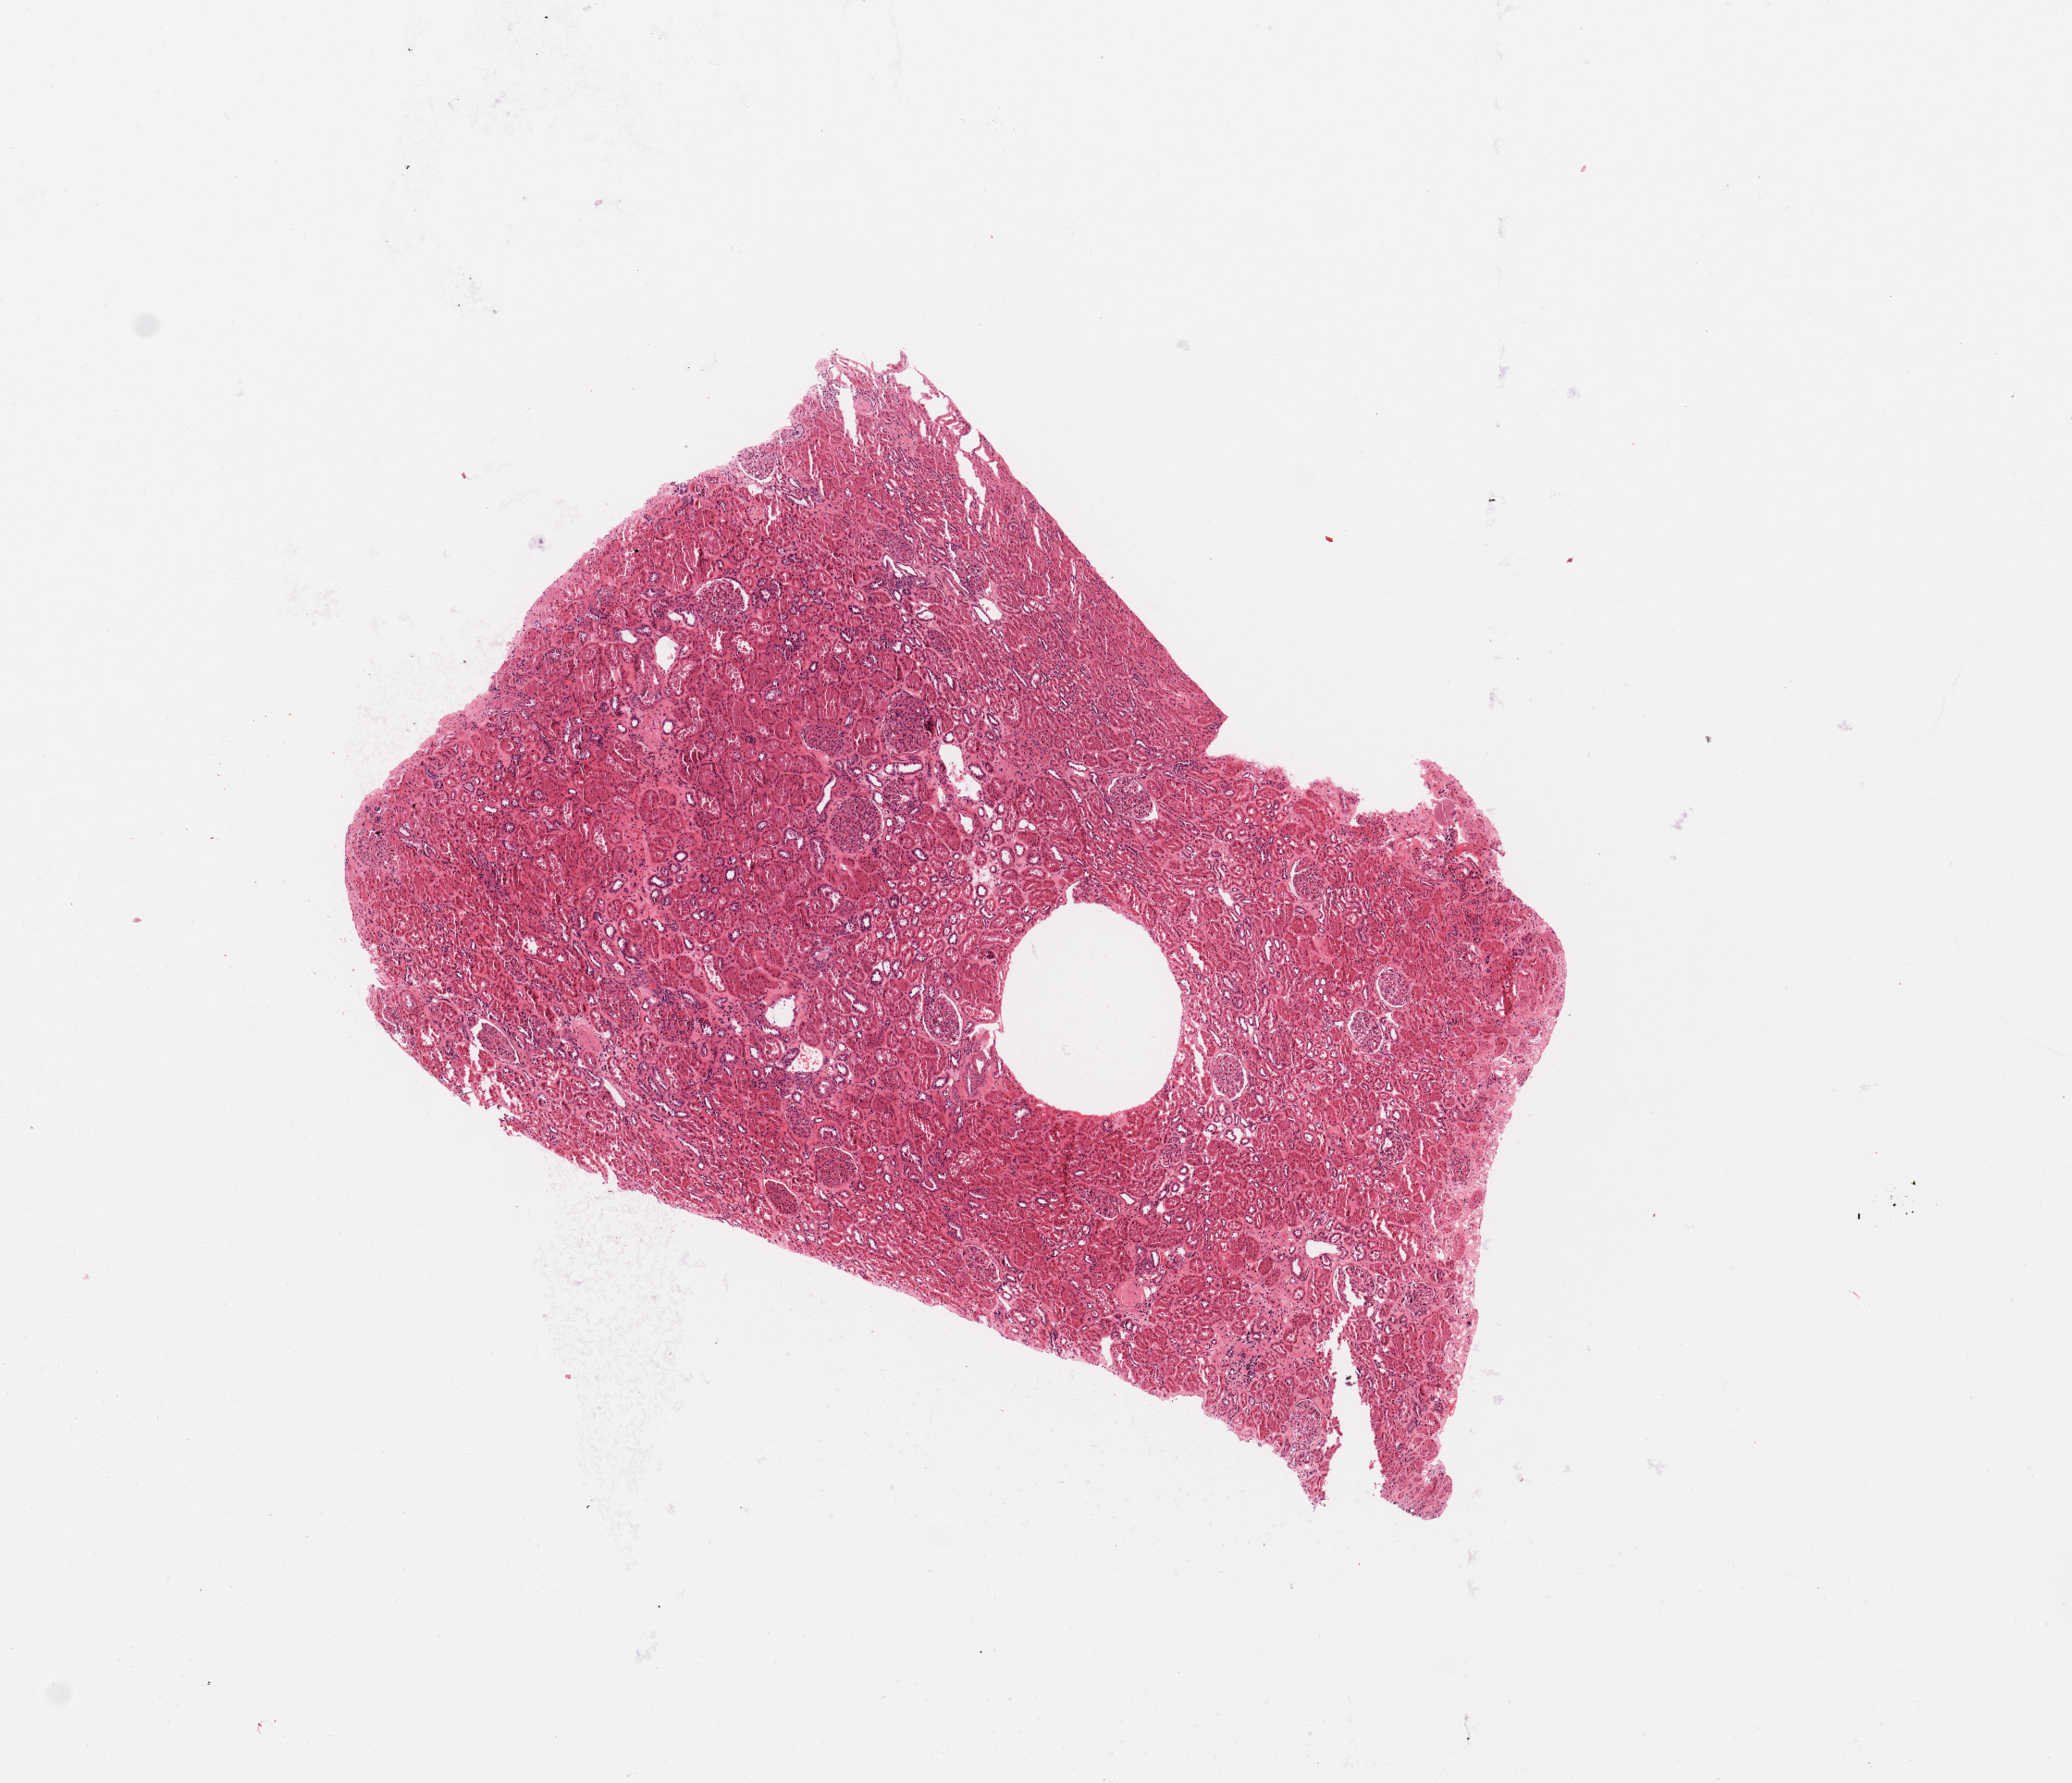
Whole-slide histology image, H&E, shown as a low-resolution overview of the whole scanned area (about 8.9 x 7.6 mm, slide scanned at 20x); kidney, normal (non-tumour) tissue. Patient: male, age 46 years.
This section: normal (non-tumour) tissue from the same patient. Patient diagnosis: Renal cell carcinoma, NOS.